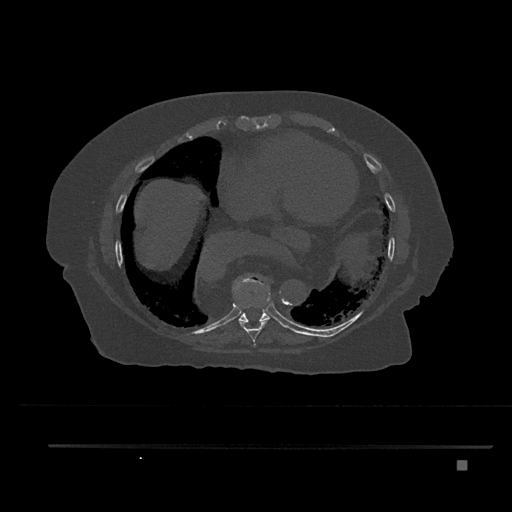
CT including the spine, one axial slice; slice 422 of 797 in the series (ordered by position); reconstruction kernel Br40s/3; bone window (W 1800 / L 400 HU); 0.5 mm slice thickness; 512 × 512 image matrix, field of view 437 × 437 mm. Patient: female, 76 years. Case-level facts recorded for this patient, not image findings: primary cancer: lung; vertebrae with lytic lesions (as recorded): T11, L3.
Annotated regions visible in this slice (semi-automatic segmentation, software-assisted and operator-edited):
- T8 vertebra: bounding box [x1, y1, x2, y2] px = [232, 283, 271, 346]
- T9 vertebra: [226, 275, 271, 324]